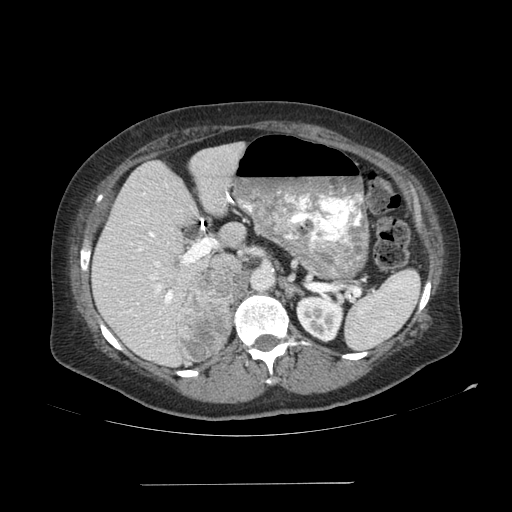
Contrast-enhanced abdominal CT, one axial slice. Slice 64 of 113 in the series (ordered by position). Soft-tissue window (W 400 / L 40 HU). 2.5 mm slice thickness. 512 × 512 image matrix, field of view 440 × 440 mm. Patient: female, 67 years. Case-level facts recorded for this patient, not image findings: diagnosis: adrenocortical carcinoma; tumour side: right adrenal; tumour size at pathology: 9.8 cm.
Outlined on this slice (semi-automatic segmentation, software-assisted and operator-edited):
- mass: bounding box <177,272,234,361> (left, top, right, bottom; pixels)